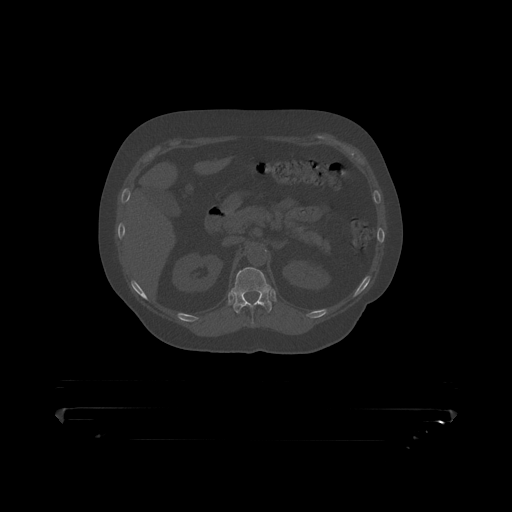
CT including the spine, one axial slice. Position 176 of 390 along the scan axis. Reconstruction kernel STANDARD. 120 kVp. Bone window (W 1800 / L 400 HU). 1.25 mm slice thickness. 512 × 512 image matrix. Male patient, age 60 years. Case-level facts recorded for this patient, not image findings: primary cancer: prostate.
Structures marked on this image (semi-automatically segmented with operator editing):
- T12 vertebra: bounding box [x1, y1, x2, y2] px = [232, 268, 272, 315]